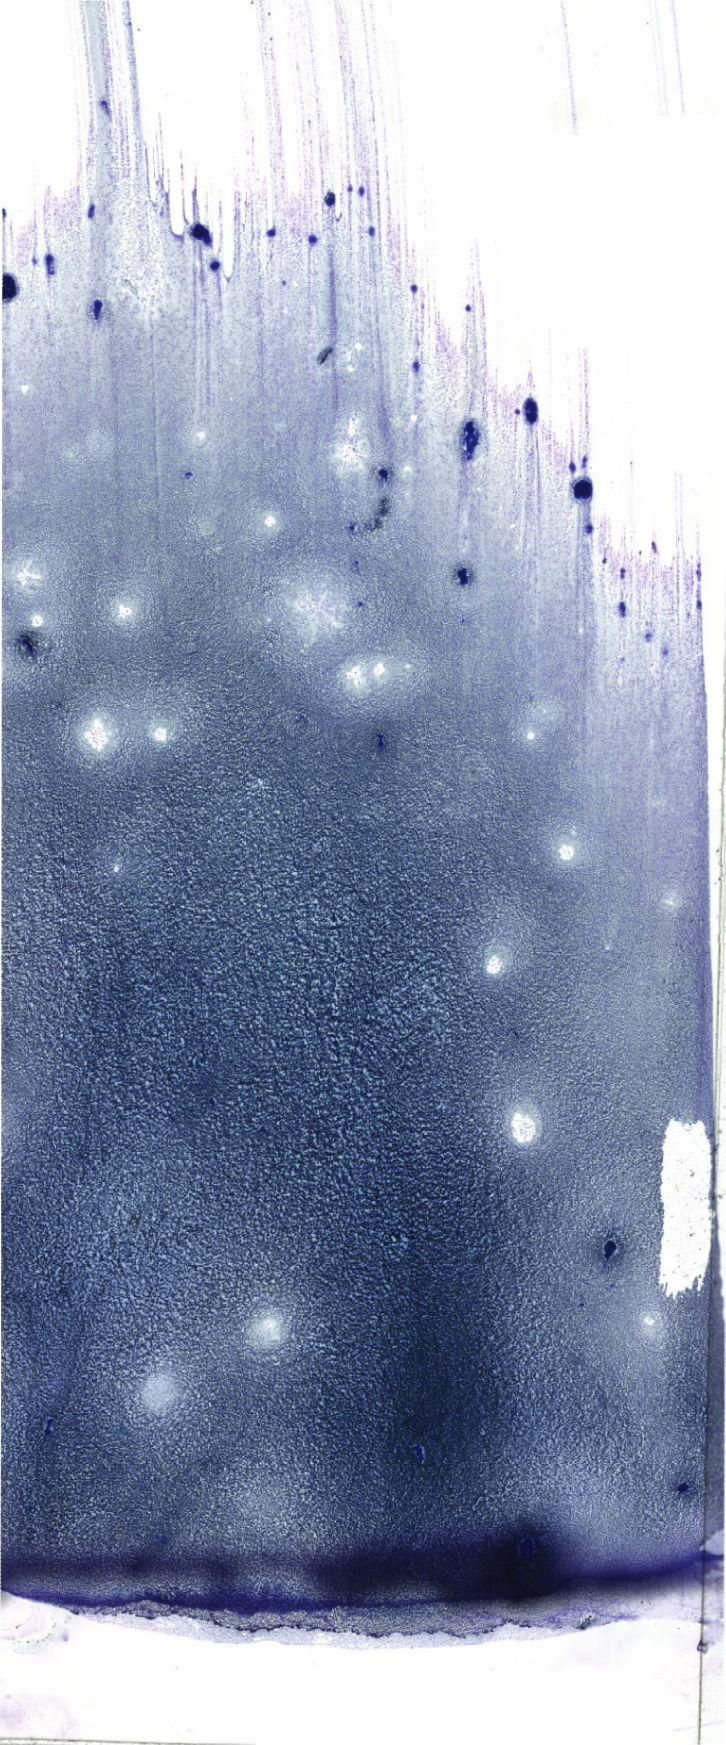
Whole-slide image of a May-Grünwald-Giemsa (MGG)-stained bone marrow aspirate smear, shown as a low-resolution overview of the whole scanned area (about 20.6 x 49.5 mm). Female patient.
Diagnosis: Acute Myelomonocytic Leukemia.